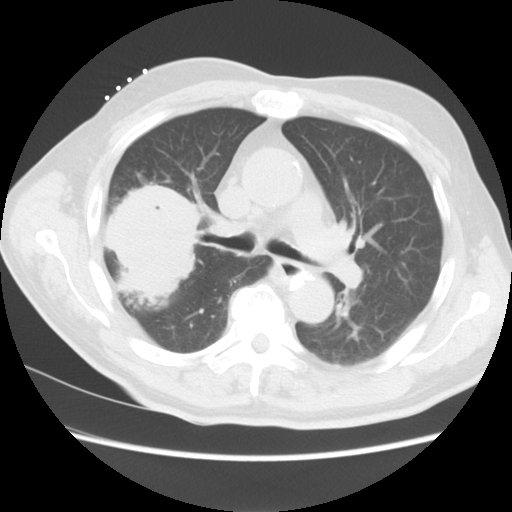
Chest CT, one axial slice; position 8 of 15 along the scan axis; reconstruction kernel STANDARD; lung window (W 1500 / L -600 HU); 512 × 512 image matrix, field of view 350 × 350 mm. Male patient, age 68 years. From the clinical record (not read from this slice): clinical TNM (as recorded): T4 N3 M0.
Structures marked on this image (rectangle marked by the reading radiologist):
- lung tumour (recorded histology: squamous cell carcinoma): bounding box <98,183,200,312> (left, top, right, bottom; pixels)